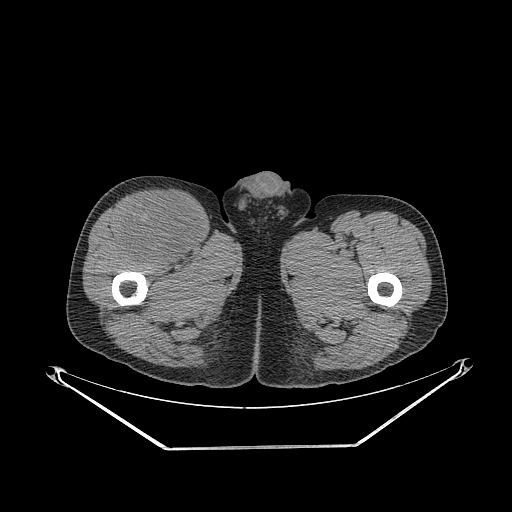
CT of an extremity soft-tissue mass (from a PET/CT study), one axial slice. Position 295 of 311 along the scan axis. 140 kVp. Soft-tissue window (W 400 / L 40 HU). 3.75 mm slice thickness. 512 × 512 image matrix, field of view 500 × 500 mm. Male patient. From the clinical record (not read from this slice): histological type: pleiomorphic leiomyosarcoma; grade: intermediate; site of the primary tumour: right thigh.
Outlined on this slice (expert contour drawn on MRI and transferred to this co-registered scan by the dataset authors):
- gross tumour volume including surrounding oedema: bounding box [x1, y1, x2, y2] px = [119, 192, 202, 264]
- gross tumour volume (mass): [121, 194, 202, 264]